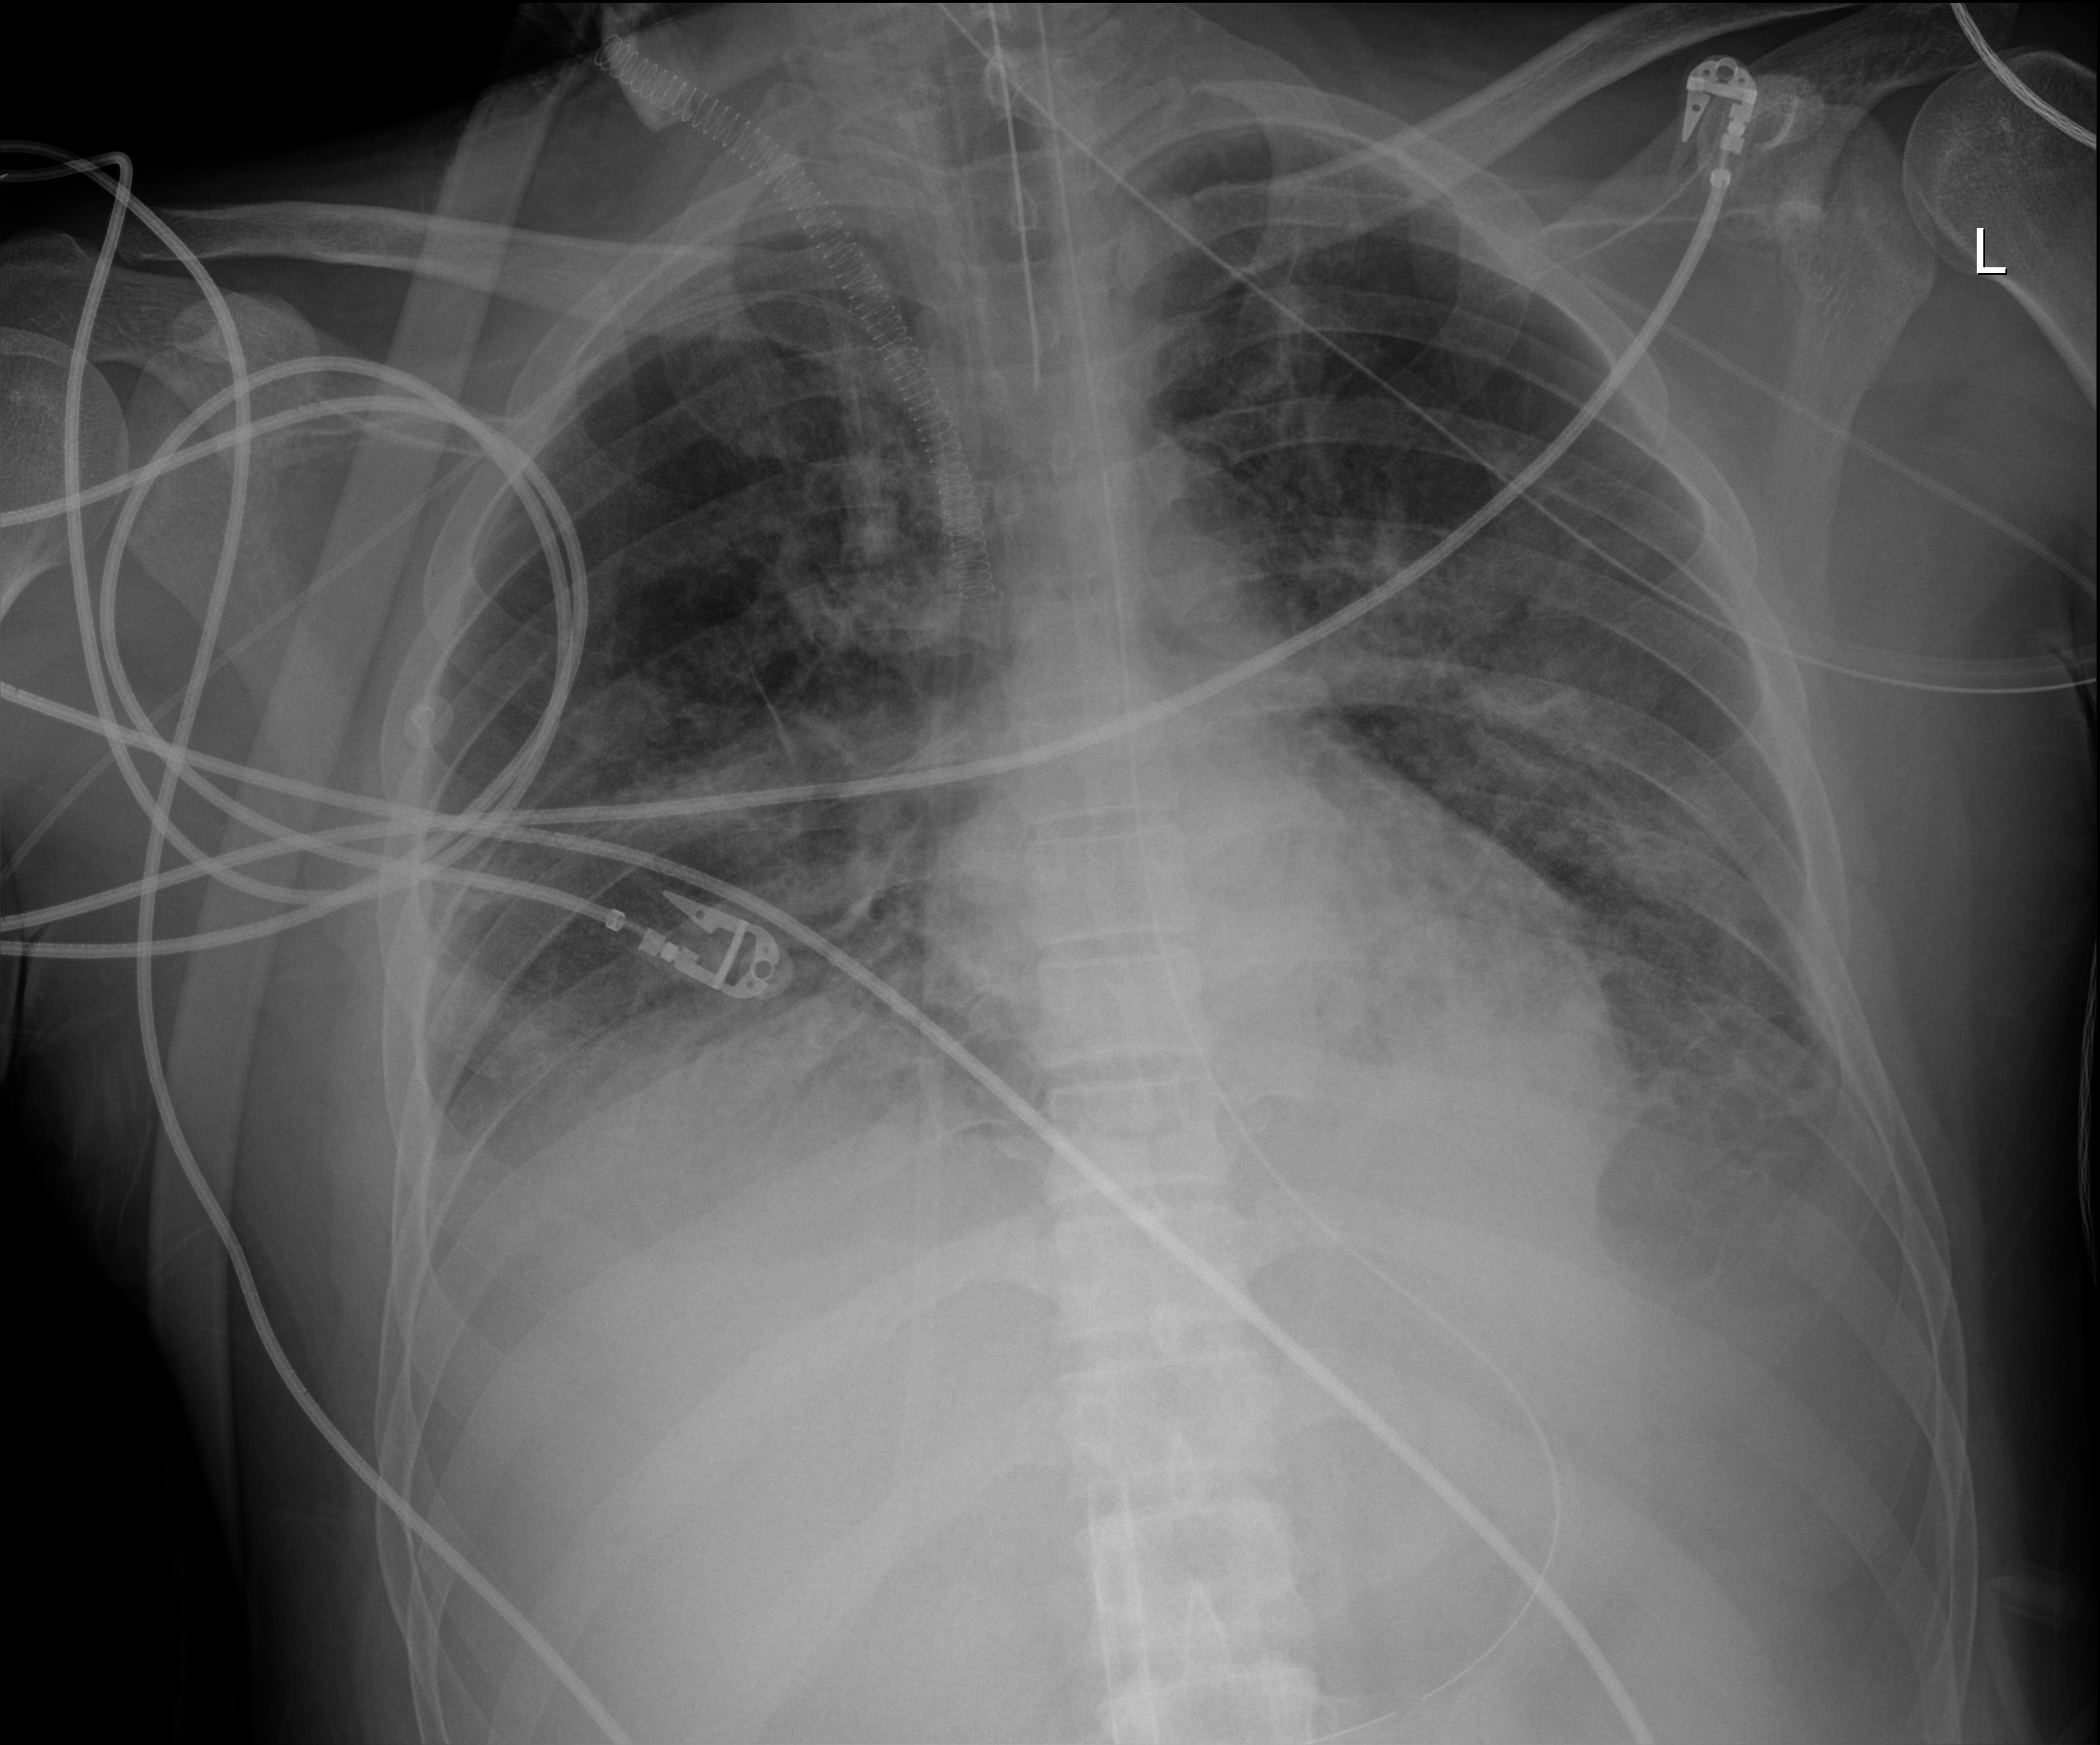
Chest X-ray (portable), anteroposterior (AP) projection. Patient hospitalised with COVID-19, aged 18–59 years.
Admission-level facts for this patient (not findings on this image; timing relative to this image not recorded): mechanically ventilated during this hospital stay: yes.